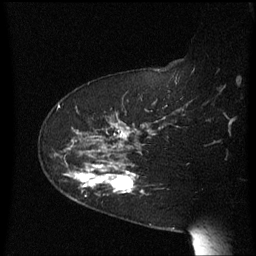
Breast MRI (dynamic contrast-enhanced), one sagittal slice. Slice 45 of 60 in the series (ordered by position). Dynamic contrast-enhanced series, image 2 of 3 at this slice position (ordered by acquisition). 1.5 T. TE 4.2 ms, TR 8.4 ms. 256 × 256 image matrix, field of view 200 × 200 mm. Female patient, age 63 years. Case-level facts recorded for this patient, not image findings: setting: breast cancer imaged before/during neoadjuvant chemotherapy; receptor status: HER2-positive.
Annotated regions visible in this slice (semi-automatically segmented with operator editing):
- analysis volume of interest (the breast-tissue region the enhancement analysis was run in; not a lesion): bounding box <64,144,145,206> (left, top, right, bottom; pixels)
- tumour enhancement mask (voxels above the 70 % enhancement threshold inside the analysis volume of interest): <74,163,136,193>